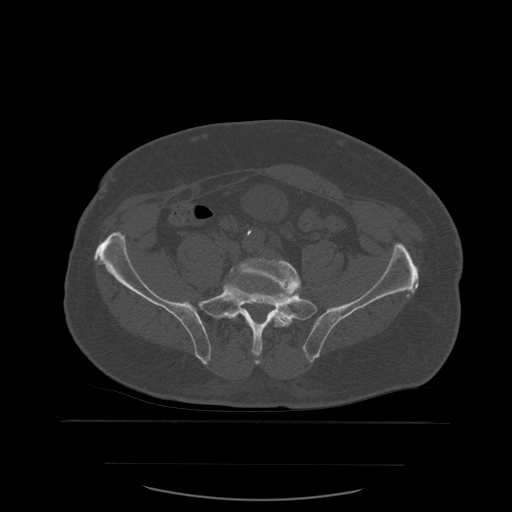
CT including the spine, one axial slice; slice 124 of 590 in the series (ordered by position); bone window (W 1800 / L 400 HU); 1.25 mm slice thickness; 512 × 512 image matrix. Patient age 71 years. From the clinical record (not read from this slice): primary cancer: lung.
Annotated regions visible in this slice (semi-automatic segmentation, software-assisted and operator-edited):
- L5 vertebra: bounding box (x1, y1, x2, y2) in pixels: (220, 259, 301, 357)